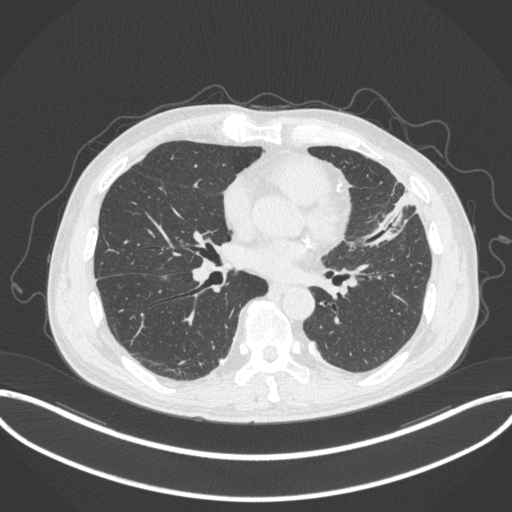
Chest CT, one axial slice; slice 152 of 382 in the series (ordered by position); reconstruction kernel B31f; 120 kVp; lung window (W 1500 / L -600 HU); 512 × 512 image matrix, field of view 415 × 415 mm. Patient: male, 64 years. Case-level facts recorded for this patient, not image findings: clinical TNM (as recorded): T4 N1 M0.
Structures marked on this image (bounding box drawn by a radiologist):
- lung tumour (recorded histology: adenocarcinoma): box from (x=365, y=190) to (x=423, y=251) px